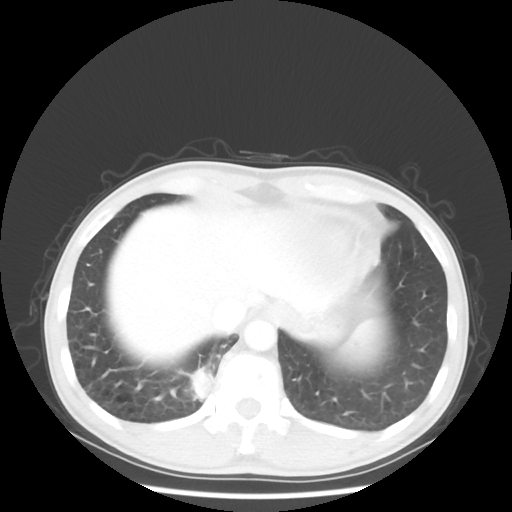
Chest CT, one axial slice. Position 8 of 58 along the scan axis. Reconstruction kernel STANDARD. 100 kVp. Lung window (W 1500 / L -600 HU). 512 × 512 image matrix, field of view 360 × 360 mm. Patient: male, 56 years. From the clinical record (not read from this slice): clinical TNM (as recorded): T2 N1 M1.
Annotated regions visible in this slice (rectangle marked by the reading radiologist):
- lung tumour (recorded histology: adenocarcinoma): bounding box <189,365,212,400> (left, top, right, bottom; pixels)